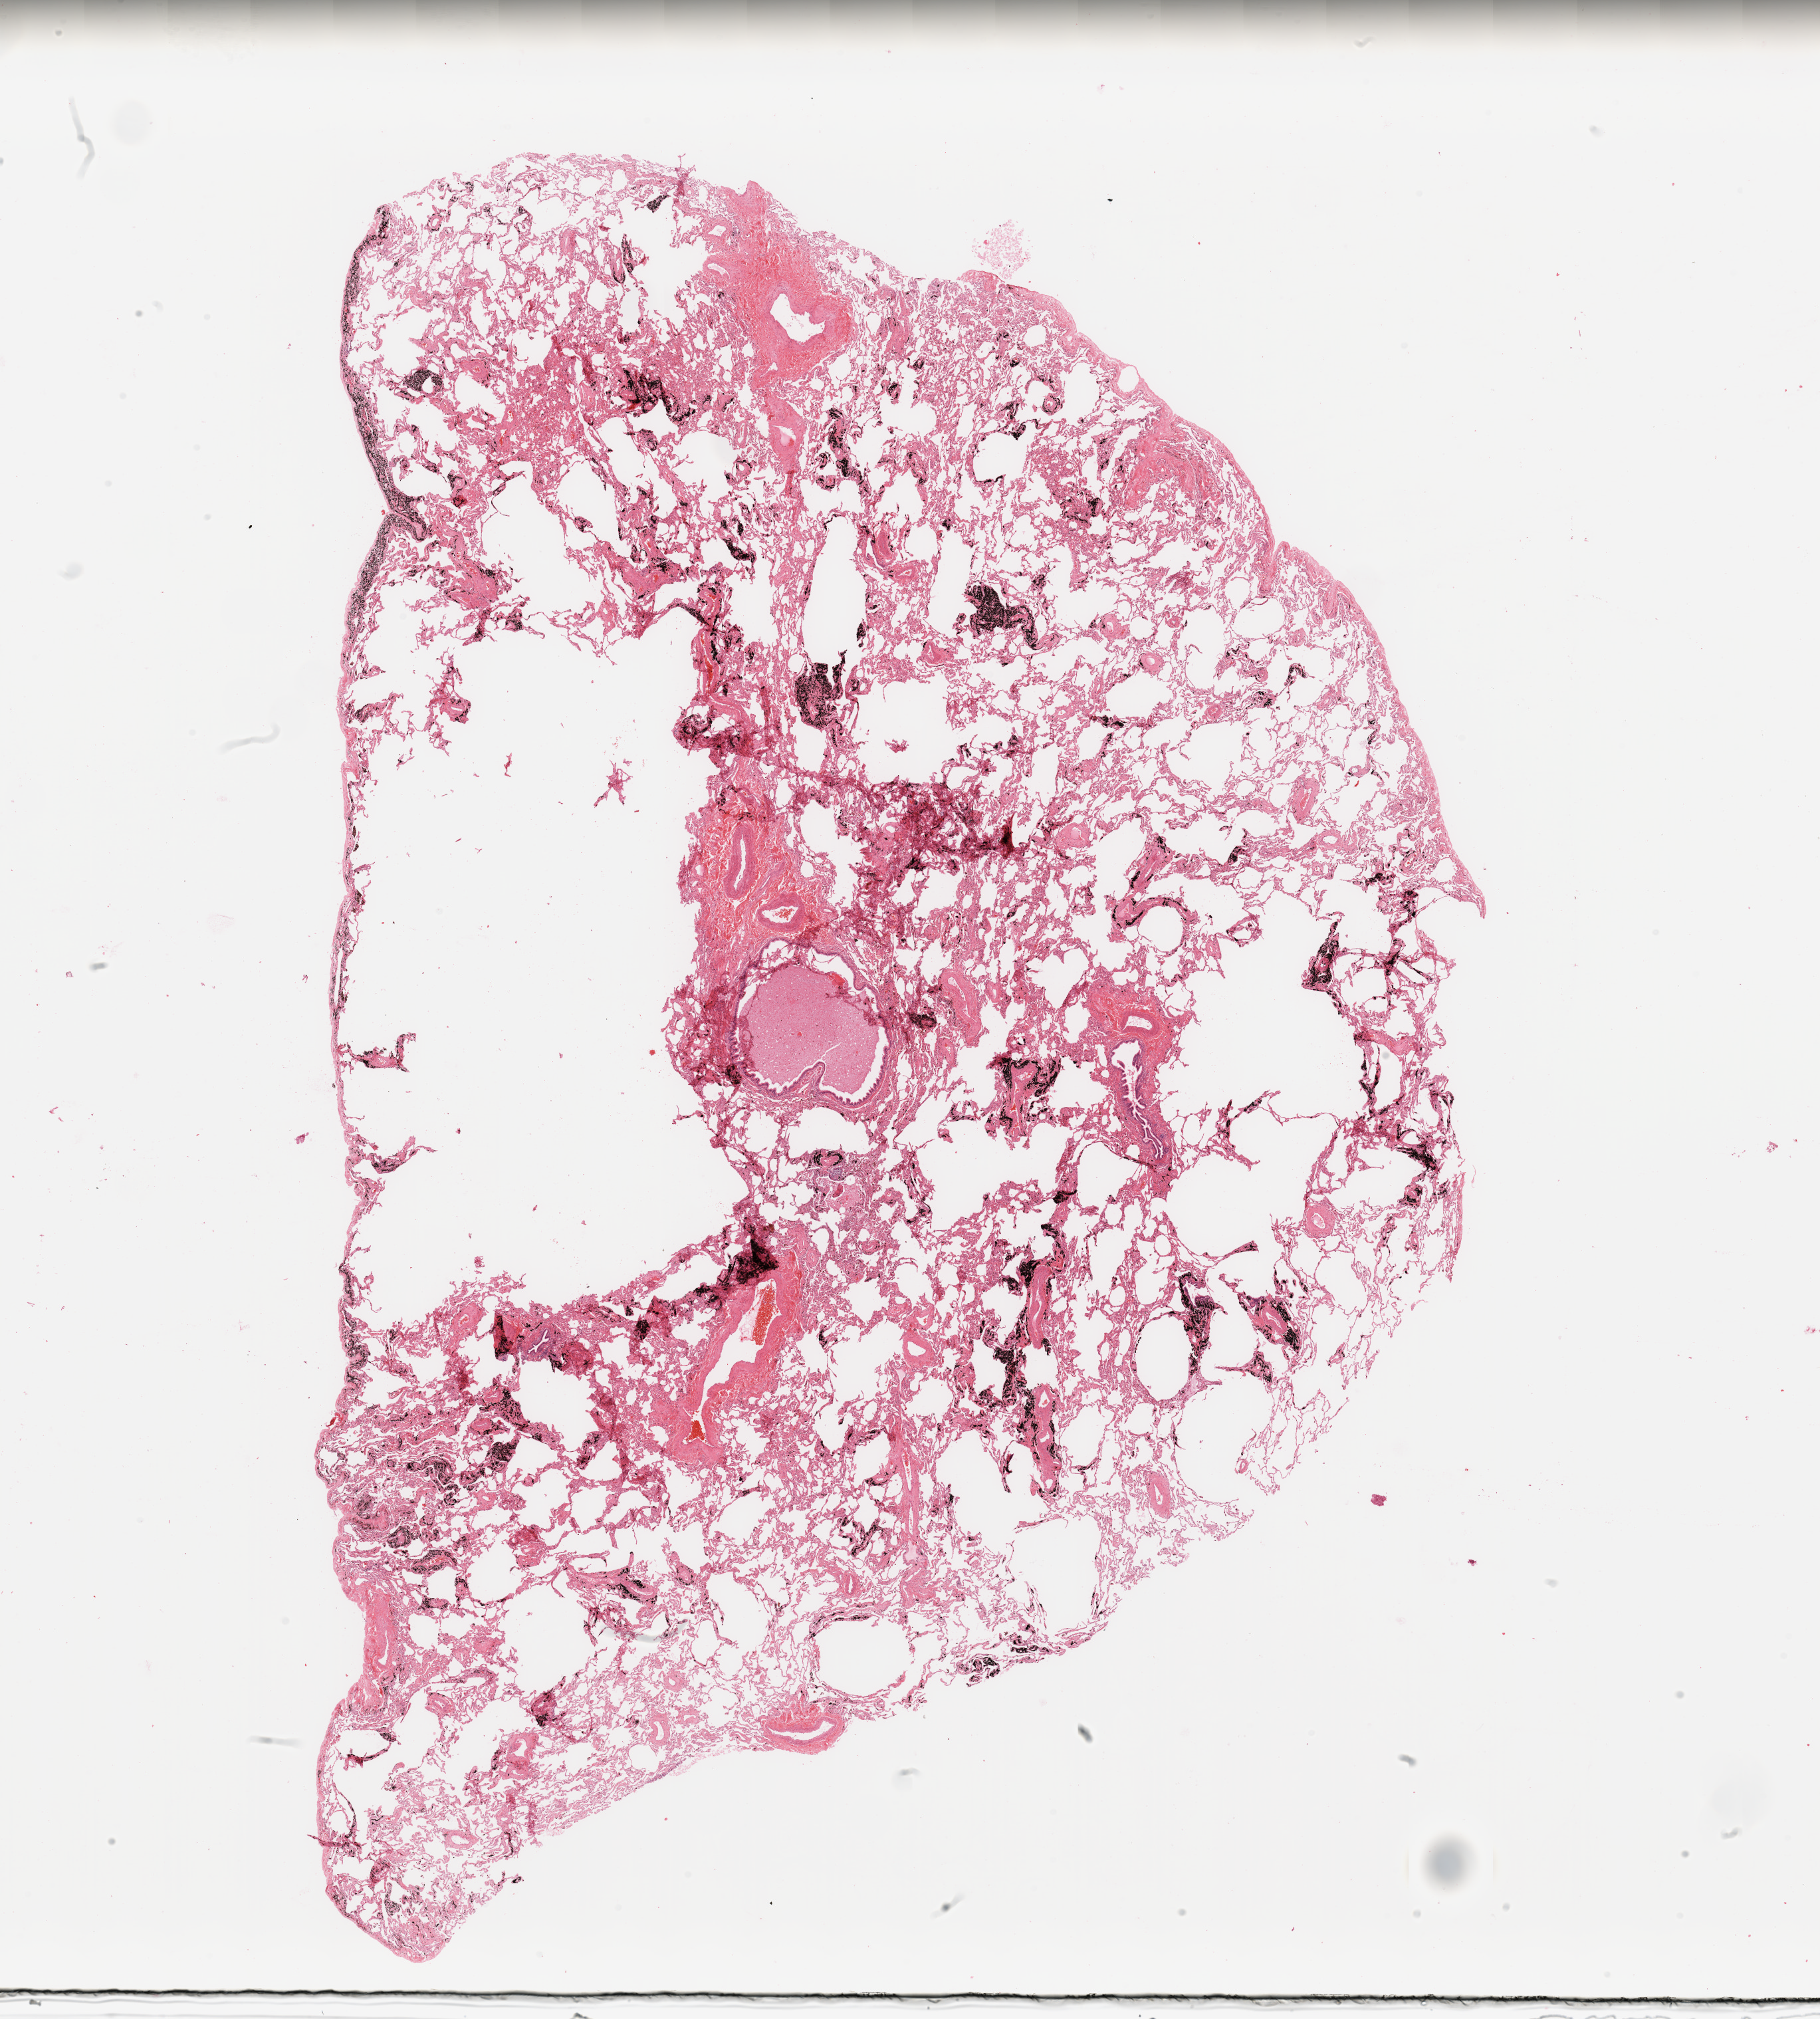
Whole-slide histology image, Hematoxylin and eosin (H&E) stained, low-resolution overview of the scanned area, about 21.7 x 24.0 mm (acquisition: 20x scan), normal (non-tumour) tissue sample, sampled site: lung. Patient: male, age 64 years.
* this section: normal (non-tumour) tissue from the same patient
* patient diagnosis: Squamous cell carcinoma, NOS